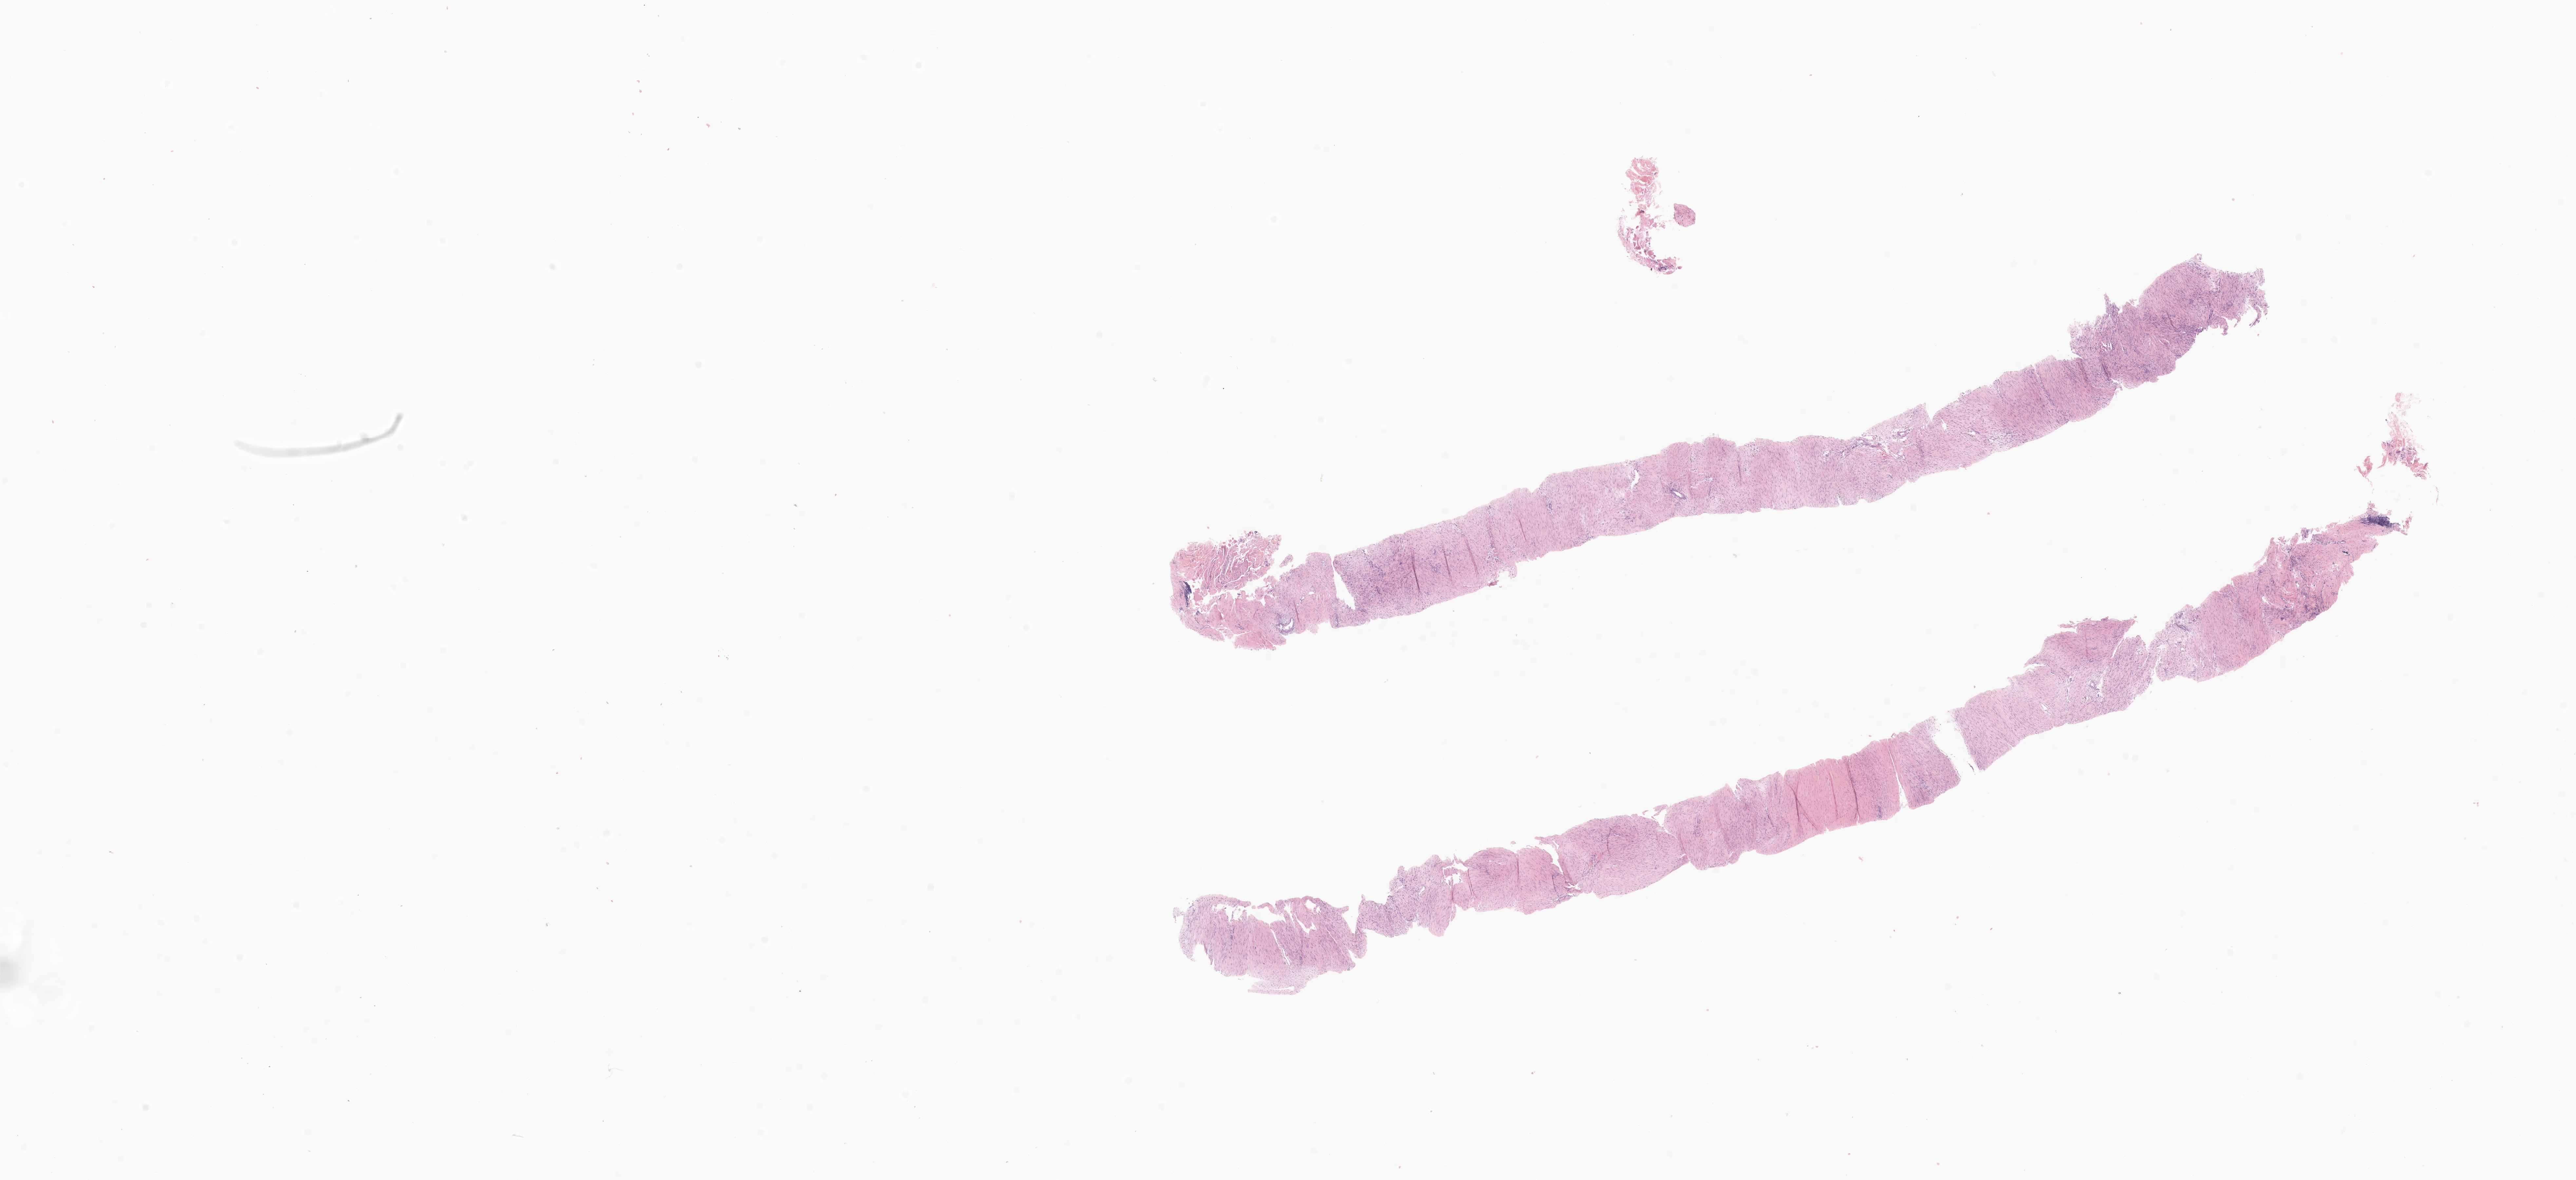
Digitized H&E-stained section of tumor tissue from the soft tissue of lower extremity — low-resolution overview of the scanned area, about 33.2 x 15.2 mm, formalin-fixed, paraffin-embedded (FFPE) tissue. Male patient, age 165 months (13 years 9 months).
Recorded diagnosis: Sclerotic fibroma.